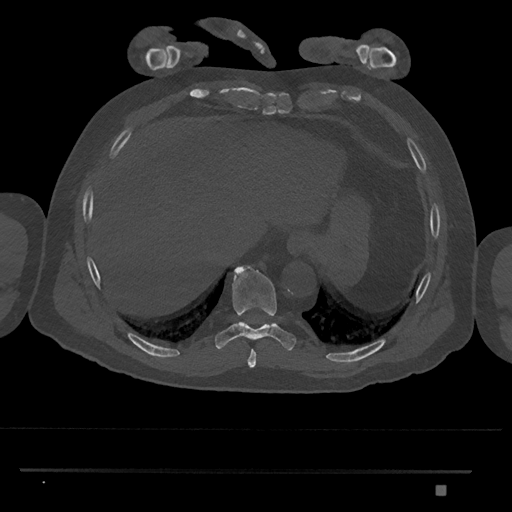
CT including the spine, one axial slice; position 1056 of 1134 along the scan axis; 120 kVp; bone window (W 1800 / L 400 HU); 512 × 512 image matrix, field of view 429 × 429 mm. Patient: male, 65 years. Case-level facts recorded for this patient, not image findings: primary cancer: prostate.
Structures marked on this image (semi-automatic segmentation, software-assisted and operator-edited):
- T8 vertebra: bounding box (x1, y1, x2, y2) in pixels: (247, 349, 257, 367)
- T9 vertebra: (215, 265, 297, 351)